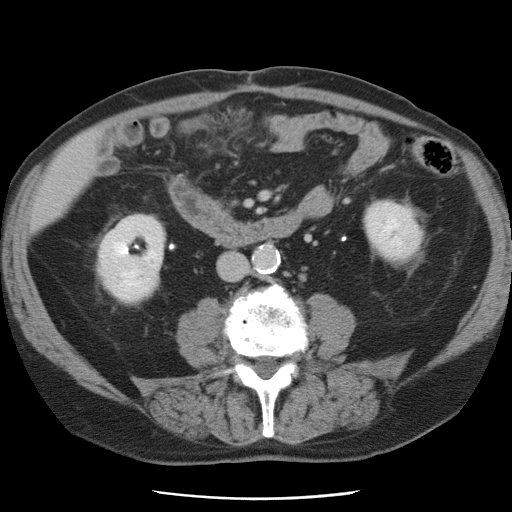
Contrast-enhanced abdominal CT, one axial slice; position 15 of 78 along the scan axis; 120 kVp; soft-tissue window (W 400 / L 40 HU); 512 × 512 image matrix. Male patient, age 75 years. From the clinical record (not read from this slice): diagnosis: colorectal cancer liver metastases, imaged before liver resection; multiple liver metastases: yes; largest metastasis: 2.4 cm.
Outlined on this slice (expert manual segmentation):
- liver: bounding box [x1, y1, x2, y2] px = [34, 136, 97, 227]
- planned liver remnant (the part of the liver to remain after resection): [34, 137, 97, 227]